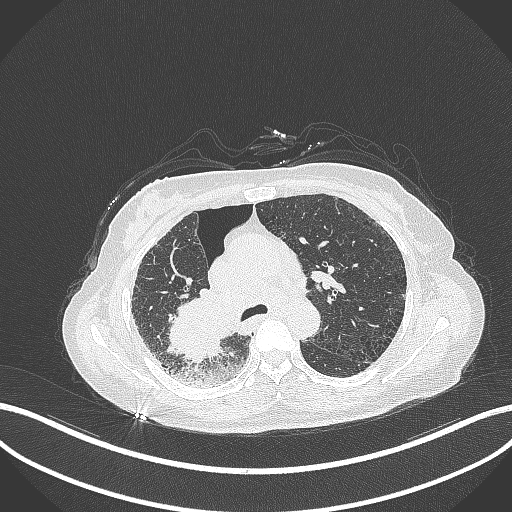
Chest CT, one axial slice. Slice 227 of 408 in the series (ordered by position). 120 kVp. Lung window (W 1500 / L -600 HU). 1 mm slice thickness. 512 × 512 image matrix. Female patient, age 64 years. Case-level facts recorded for this patient, not image findings: clinical TNM (as recorded): T3 N3 M0.
Structures marked on this image (bounding box drawn by a radiologist):
- lung tumour (recorded histology: squamous cell carcinoma): bounding box (x1, y1, x2, y2) in pixels: (165, 283, 239, 368)